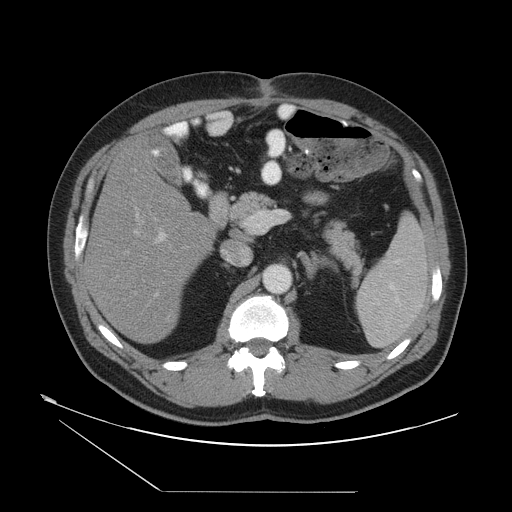
Contrast-enhanced abdominal CT, one axial slice. Slice 25 of 55 in the series (ordered by position). Reconstruction kernel STANDARD. 120 kVp. Intravenous contrast given. Soft-tissue window (W 400 / L 40 HU). 512 × 512 image matrix, field of view 454 × 454 mm. Male patient, age 59 years. Case-level facts recorded for this patient, not image findings: diagnosis: colorectal cancer liver metastases, imaged before liver resection; multiple liver metastases: yes.
Annotated regions visible in this slice (manually delineated by an expert):
- hepatic veins: bounding box [x1, y1, x2, y2] px = [125, 200, 146, 295]
- liver: [87, 139, 215, 345]
- planned liver remnant (the part of the liver to remain after resection): [88, 139, 216, 345]
- portal vein (with intrahepatic branches): [154, 219, 166, 297]